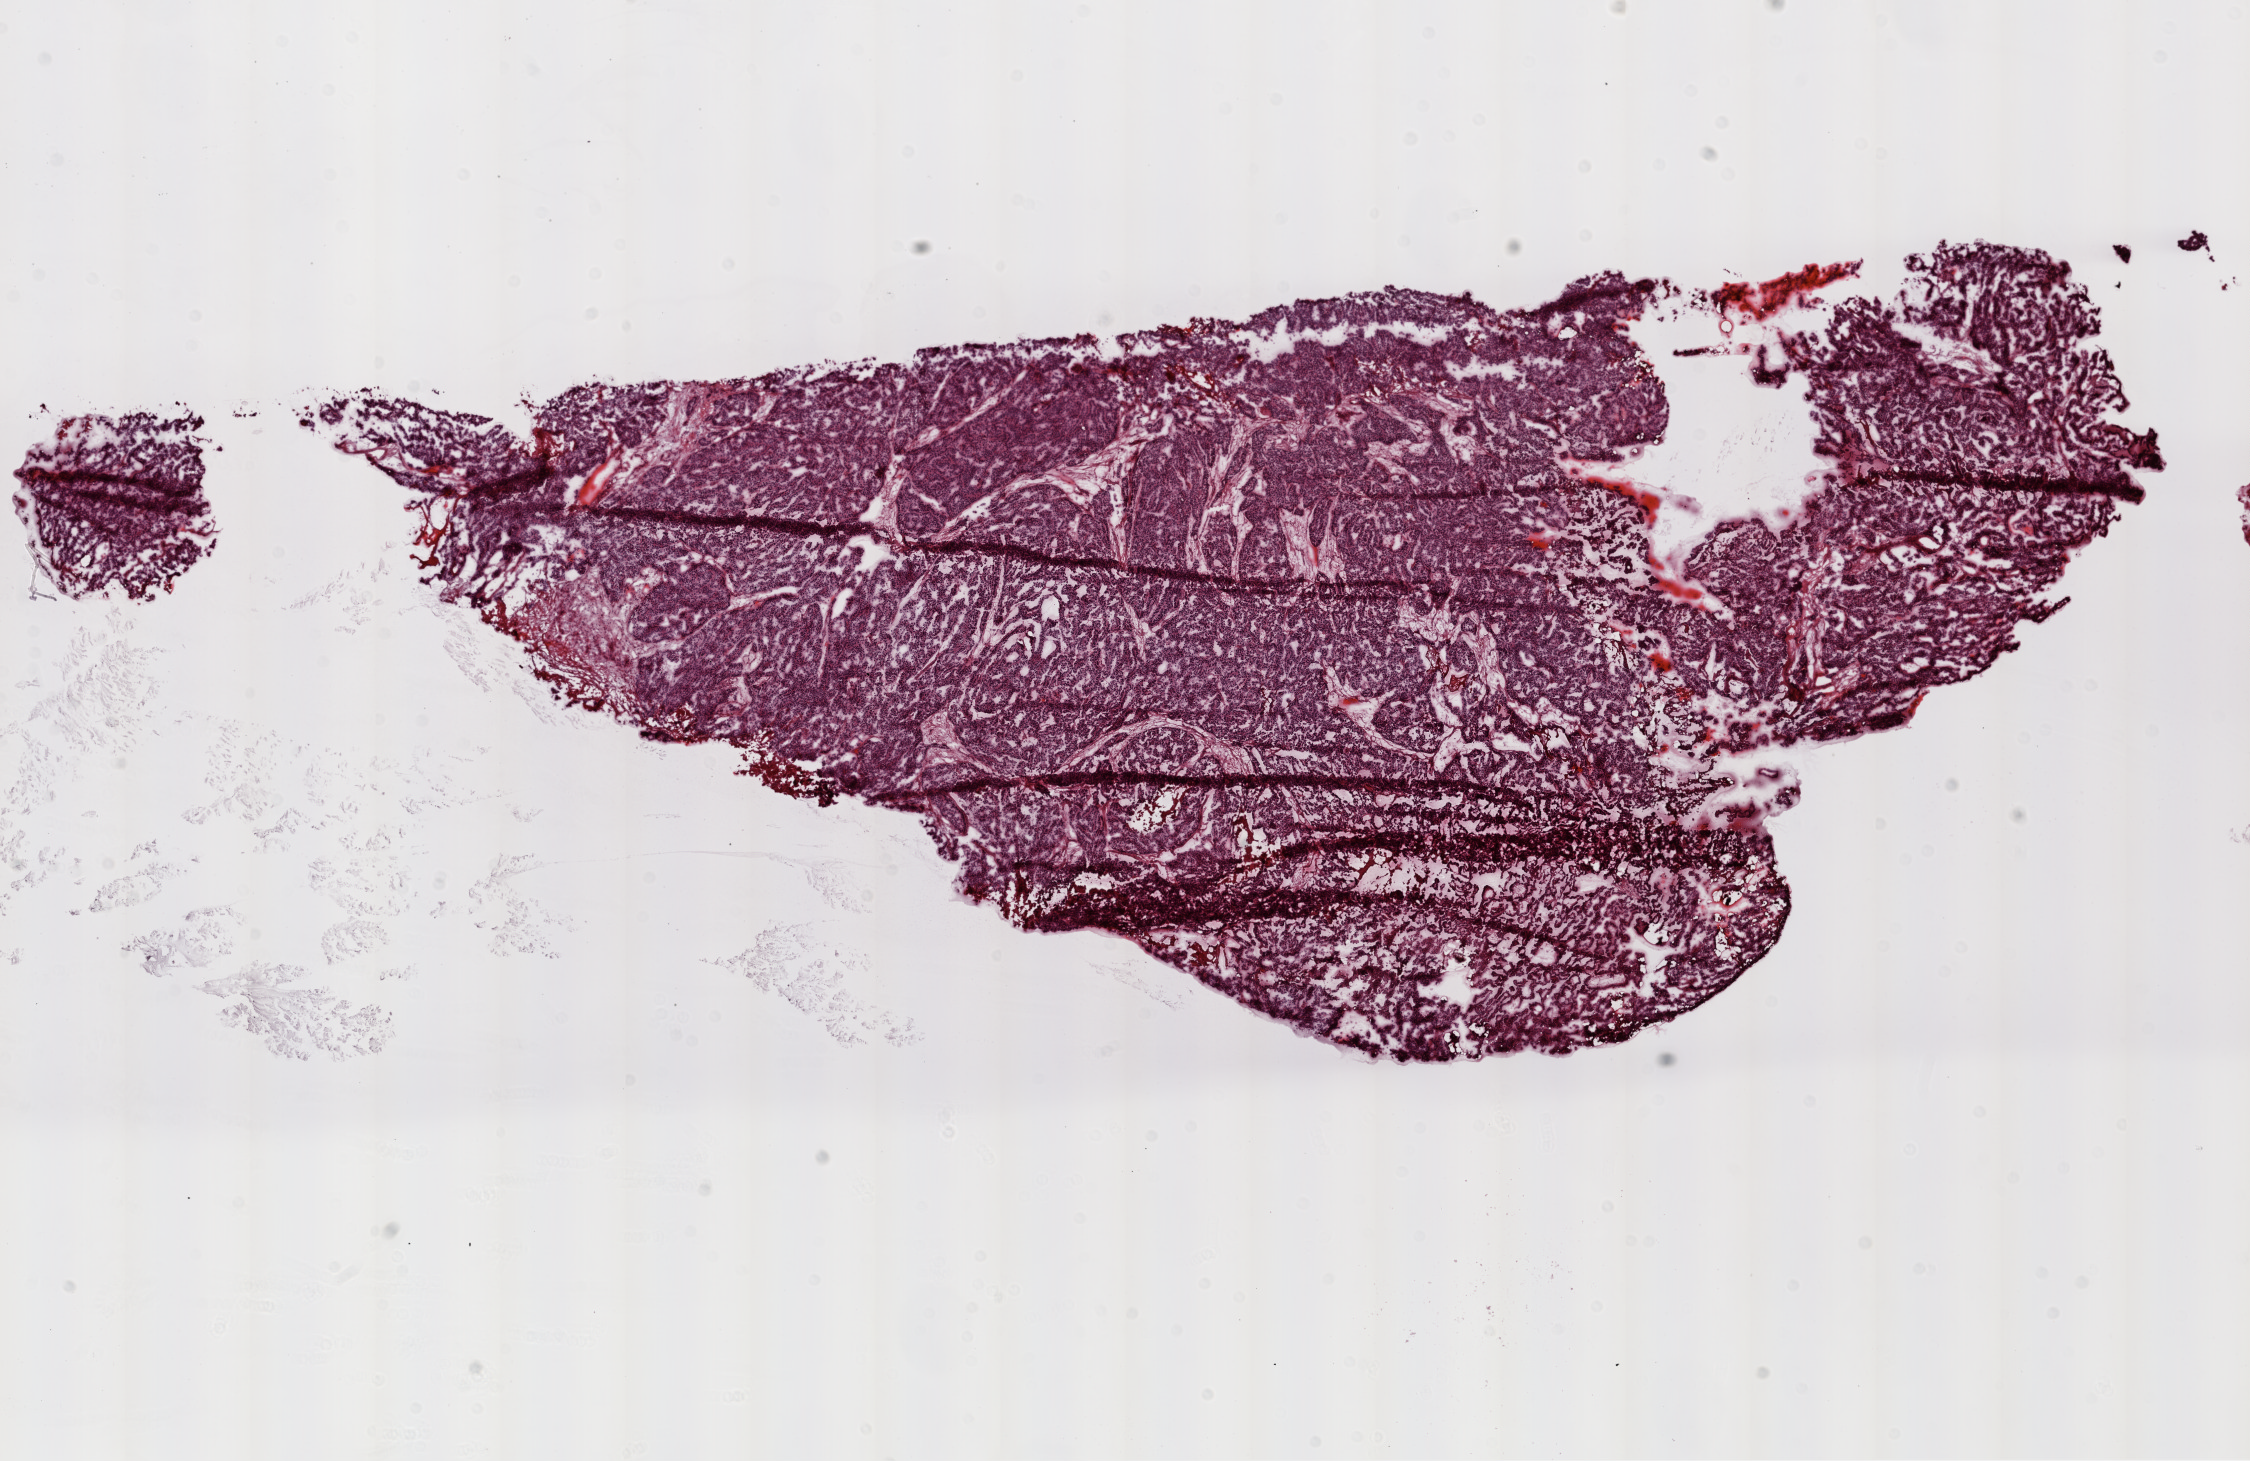
H&E-stained whole-slide image, a low-resolution overview of the entire scanned area, about 18.1 x 11.7 mm; frozen section from the top of the tissue portion; primary tumour sample from the ovary. Patient: female, age at initial diagnosis 67 years. Histologic grade: G3 (poorly differentiated). Pathologist review of this section (percent, as recorded): tumour cells 100%, tumour nuclei 95%, normal cells 0%, stromal cells 0%, necrosis 0%. Infiltration values recorded for this section: lymphocyte infiltration 0%, monocyte infiltration 0%, neutrophil infiltration 0%.
Histologic diagnosis: Serous cystadenocarcinoma, NOS. FIGO stage: IIIC.